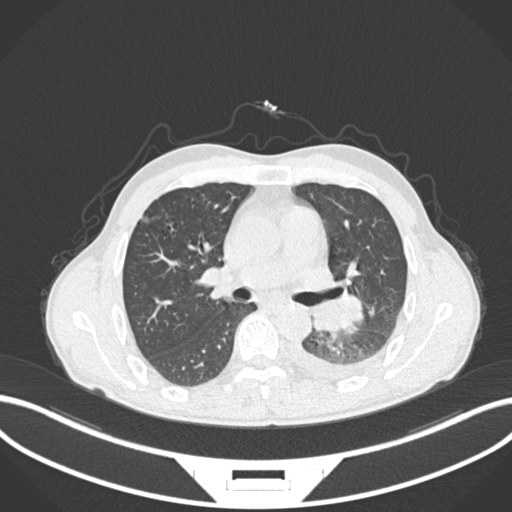
Chest CT, one axial slice; position 145 of 222 along the scan axis; 120 kVp; lung window (W 1500 / L -600 HU); 1 mm slice thickness; 512 × 512 image matrix, field of view 400 × 400 mm. Patient: male, 47 years. Case-level facts recorded for this patient, not image findings: clinical TNM (as recorded): T3 N1 M1c.
Outlined on this slice (bounding box drawn by a radiologist):
- lung tumour (recorded histology: small cell carcinoma): bounding box [x1, y1, x2, y2] px = [306, 293, 370, 336]